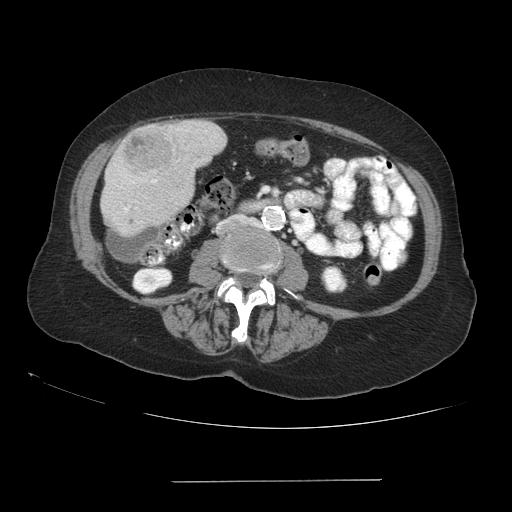
Contrast-enhanced abdominal CT (liver protocol), one axial slice; slice 24 of 89 in the series (ordered by position); reconstruction kernel STANDARD; soft-tissue window (W 400 / L 40 HU); 512 × 512 image matrix. From the clinical record (not read from this slice): diagnosis: hepatocellular carcinoma (patient treated with transarterial chemoembolisation; whether this scan precedes or follows treatment is not stated here); TNM stage (as recorded): Stage-IVA; Child-Pugh class: A; tumour differentiation: poorly differentiated; tumour nodularity: uninodular.
Outlined on this slice (semi-automatic segmentation, software-assisted and operator-edited):
- liver parenchyma outside the tumour (the mass and vessels are separate outlines, so this box may not span the whole liver): bounding box (x1, y1, x2, y2) in pixels: (100, 120, 226, 236)
- mass: (124, 128, 170, 172)
- liver vessels: (125, 180, 156, 211)